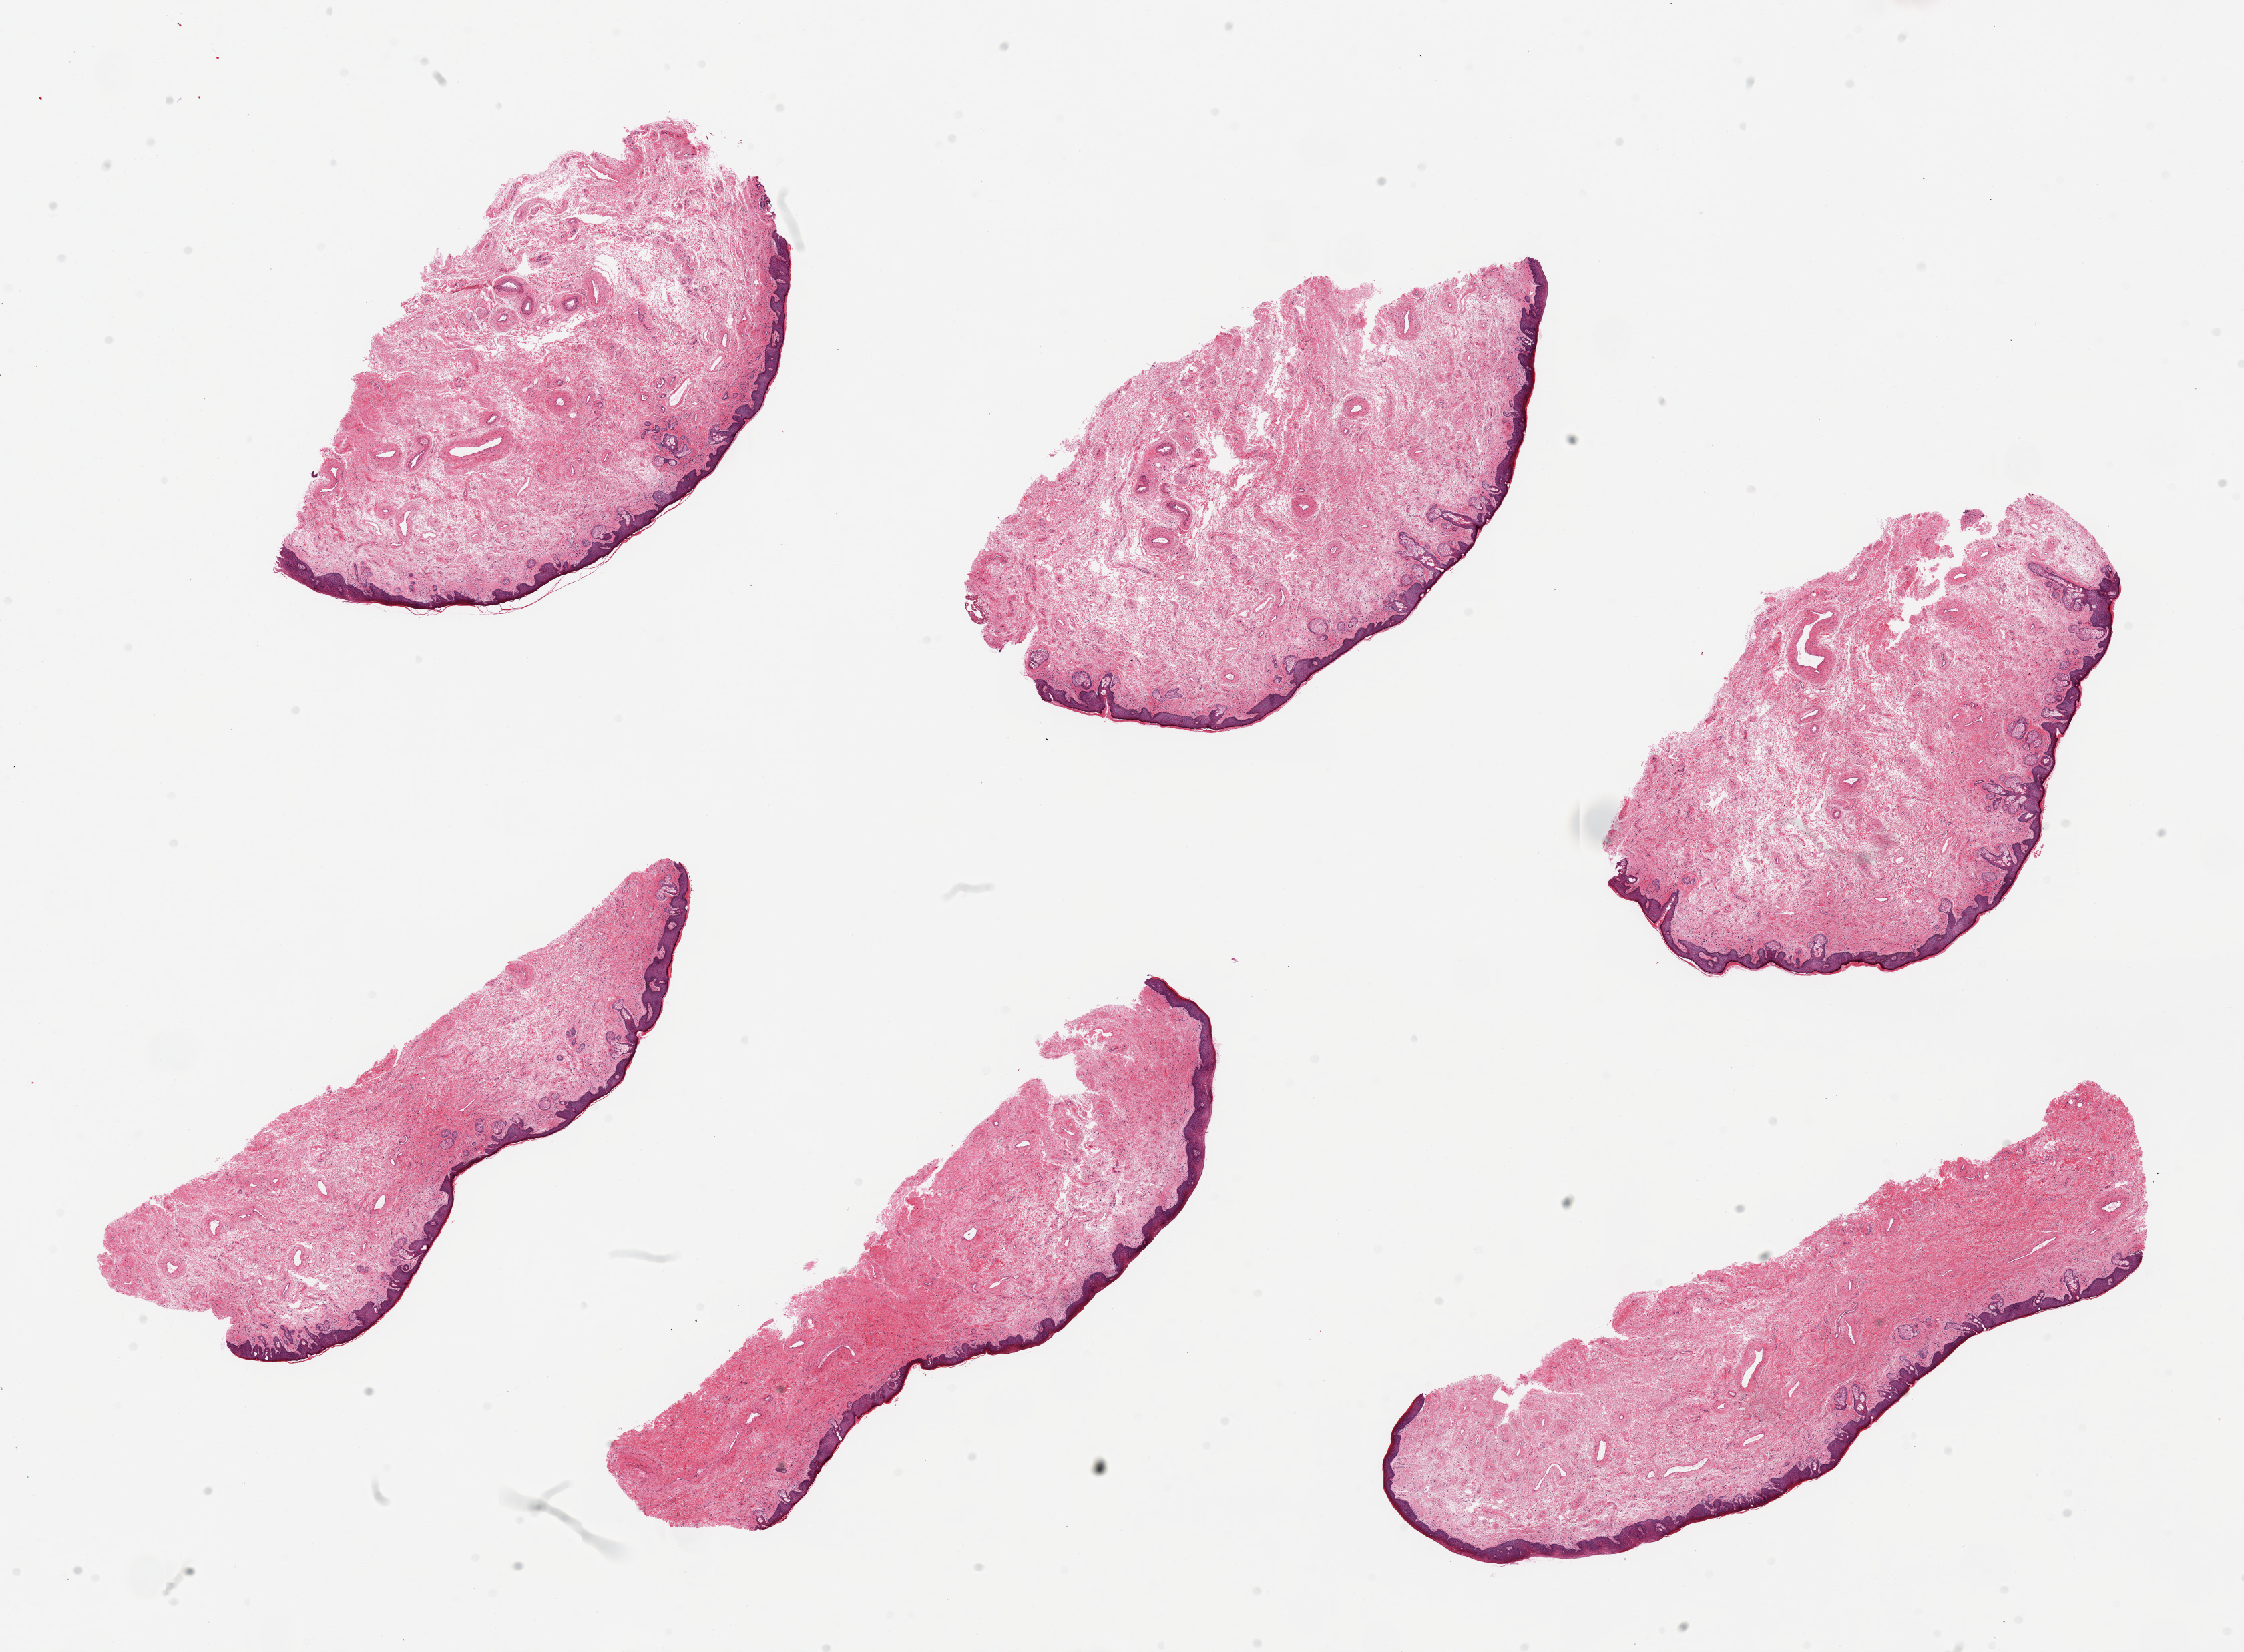
Hematoxylin and eosin (H&E) whole-slide image — shown as a low-resolution overview of the whole scanned area (about 26.6 x 19.6 mm, acquisition: 20x scan); PAXgene-fixed, paraffin-embedded tissue; section of vagina (target tissue); donor tissue sample. Female donor.
Reviewer comment on this tissue sample: 6 pieces, numerous sebaceous glands indicating vulva was sampled.